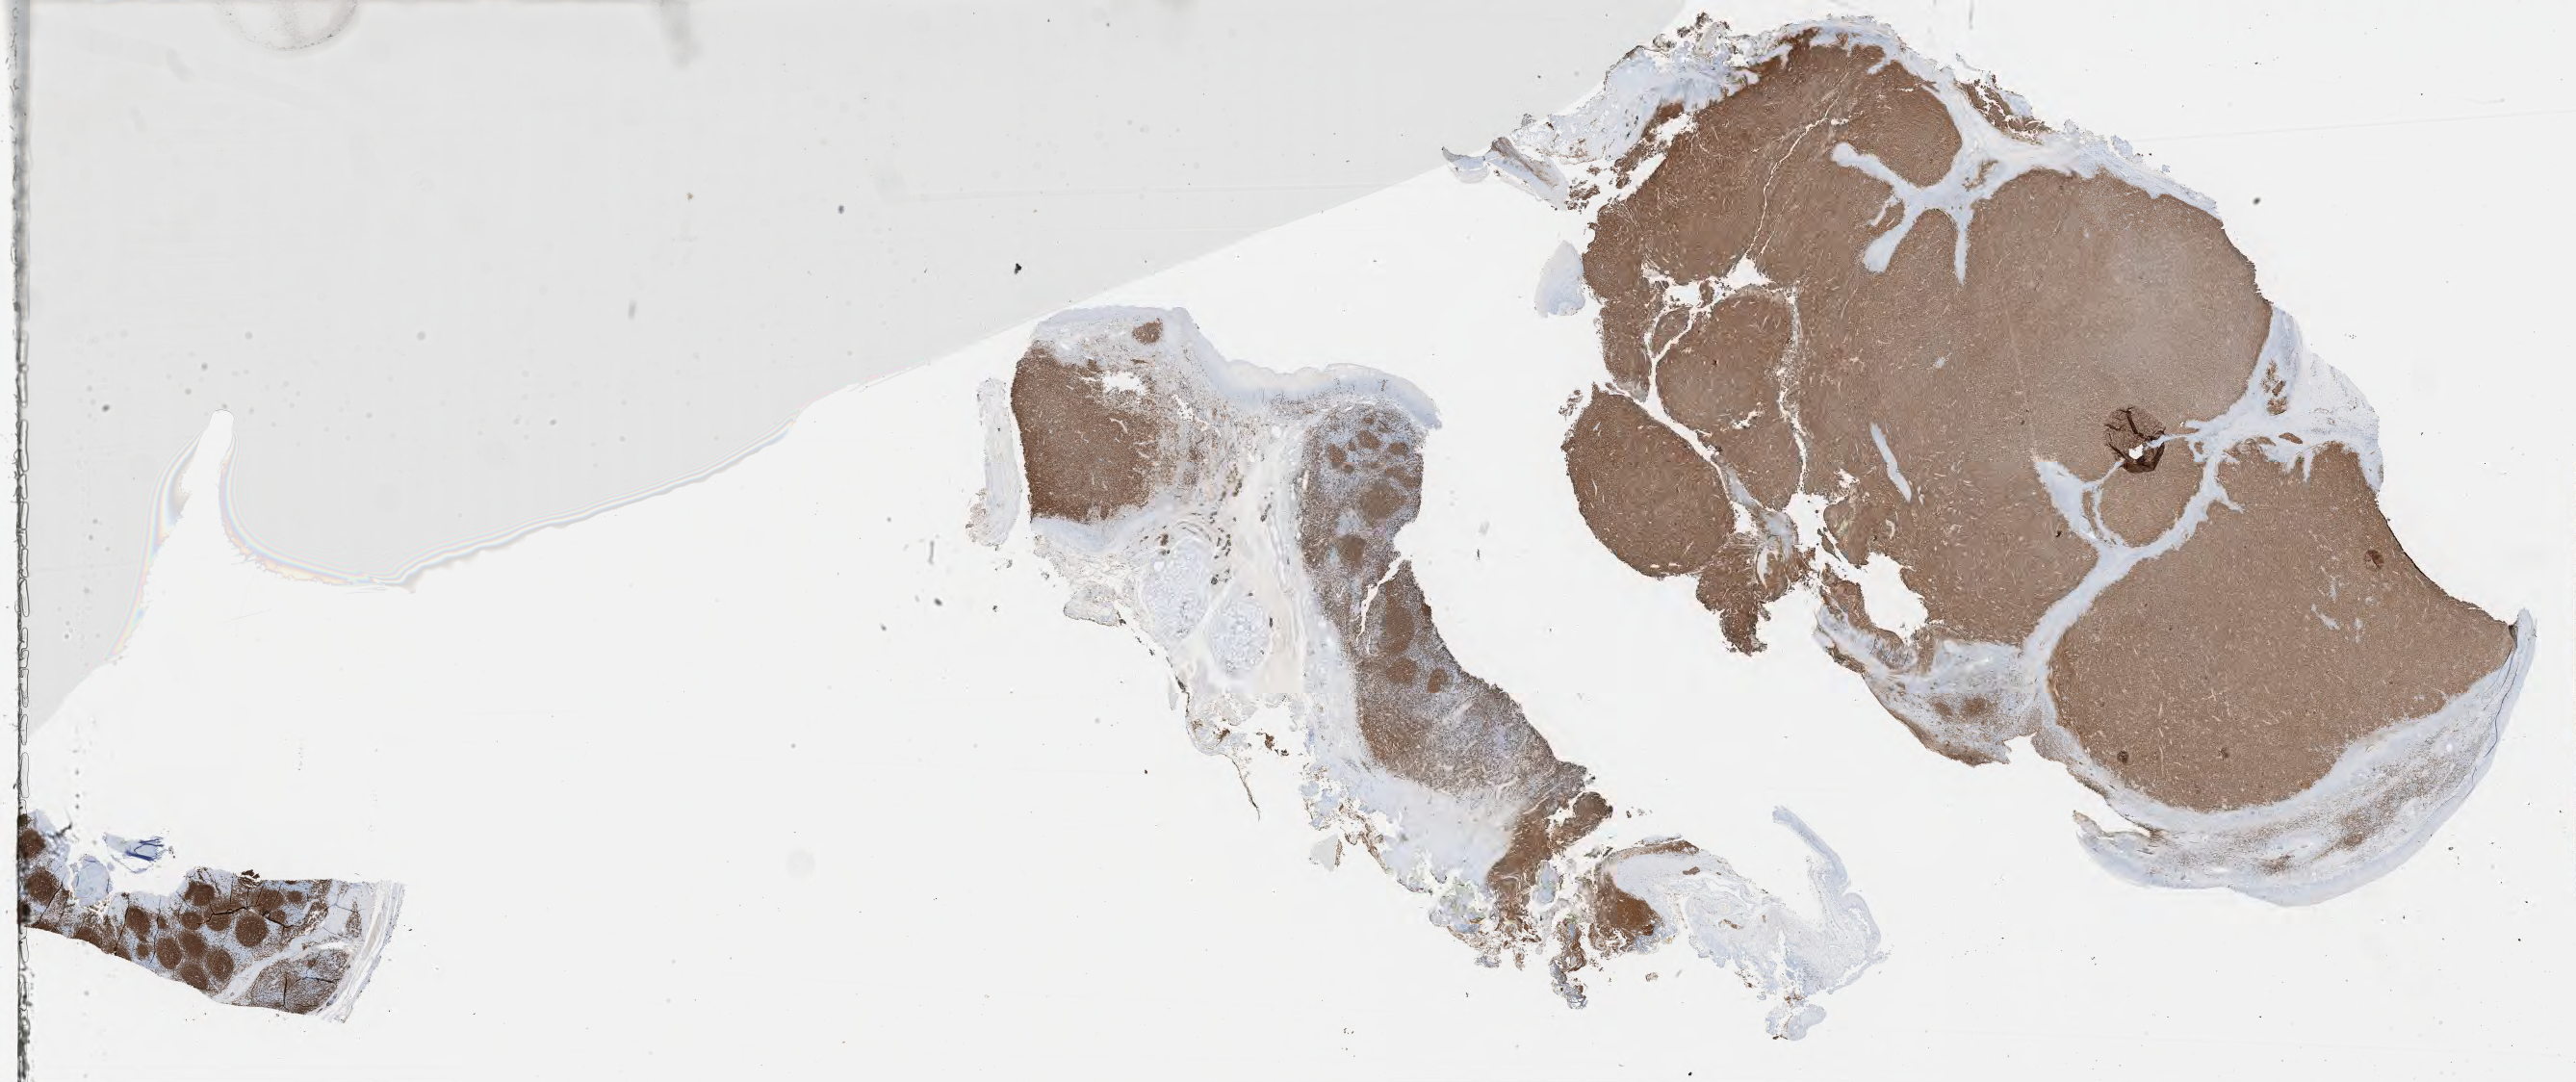
Immunohistochemistry (IHC) whole-slide image stained for CD20, a low-resolution overview of the entire scanned area, about 43.3 x 18.2 mm. Specimen: tumor tissue. Site: lymph node. Male patient, 56 years old.
Diagnosis: Diffuse large B-cell lymphoma, NOS.